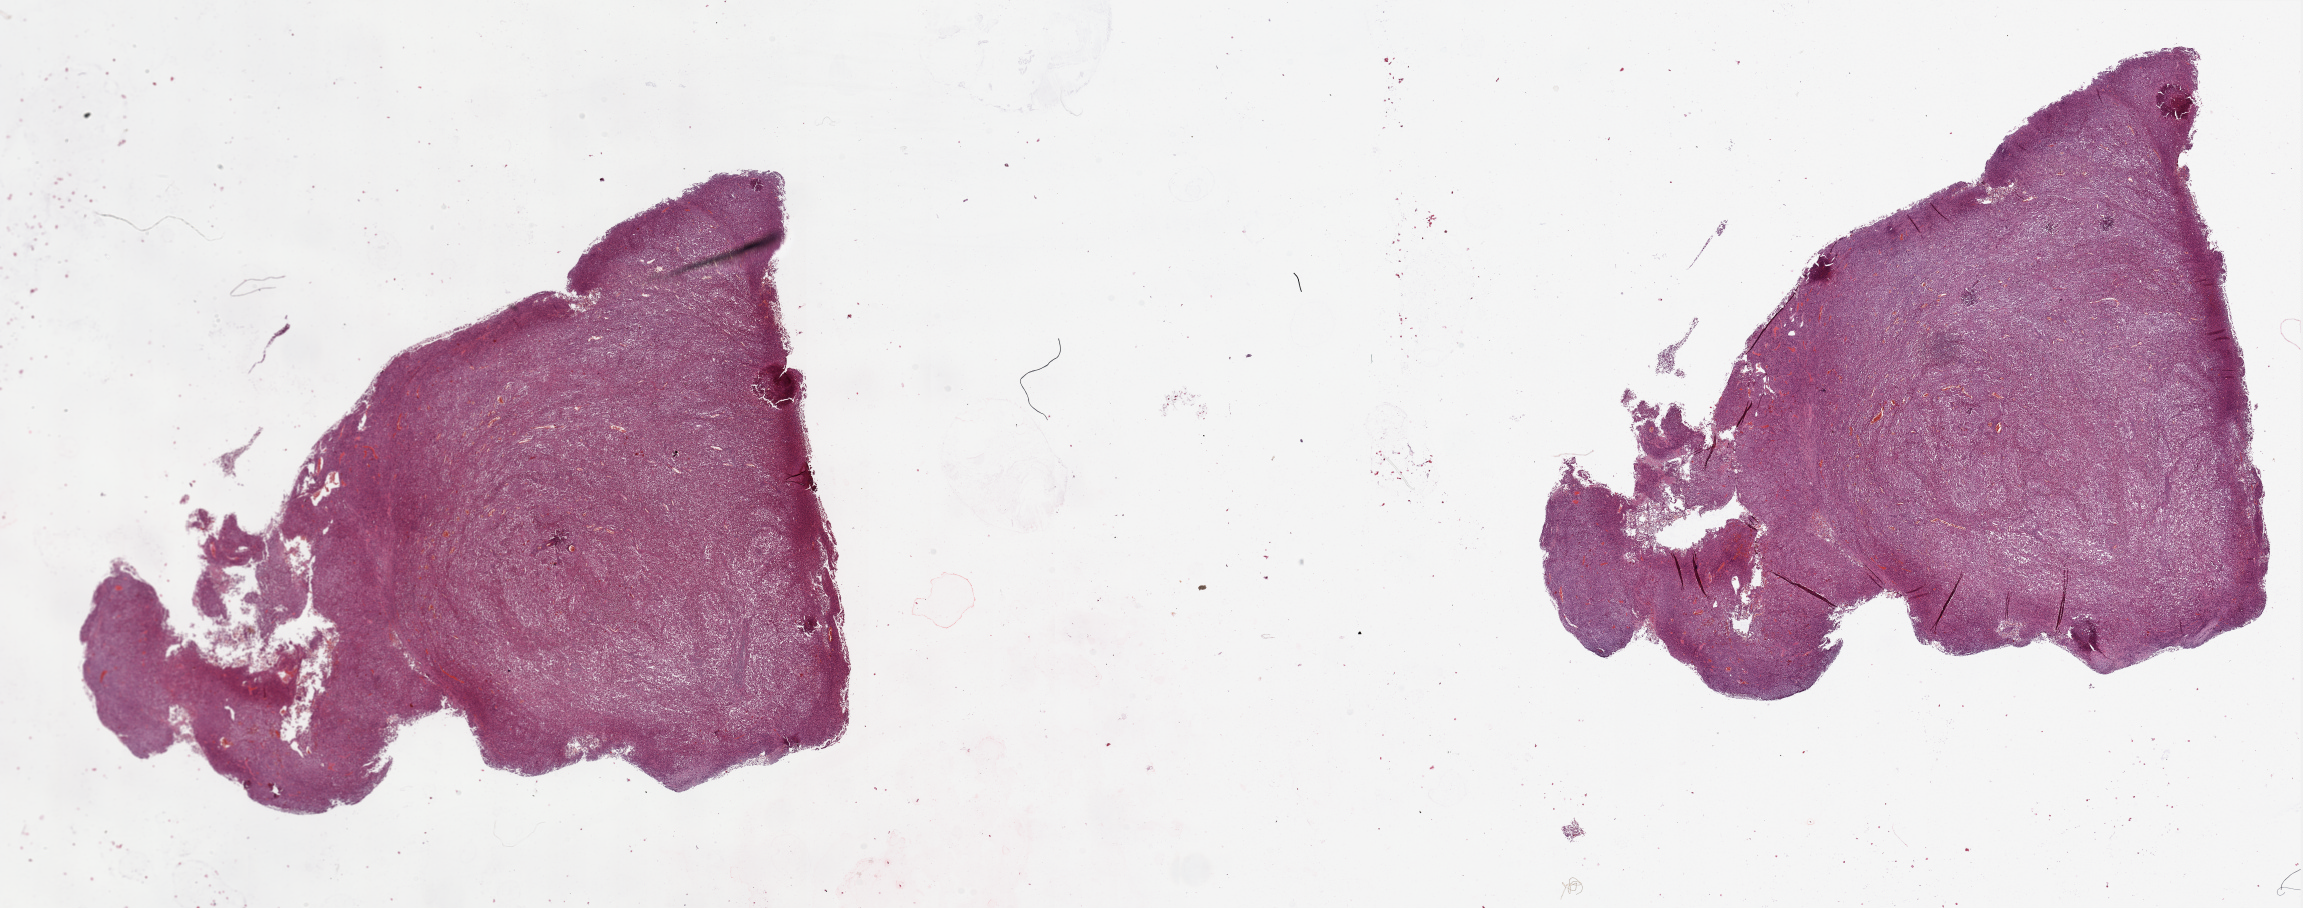
Hematoxylin and eosin (H&E) stained whole-slide image — low-resolution overview of the scanned area, about 36.4 x 14.4 mm; tumour tissue sample, lung. Patient: male, age 56 years. Histologic grade: G3 (poorly differentiated).
• diagnosis: Adenocarcinoma, NOS
• AJCC pathologic stage: IIA